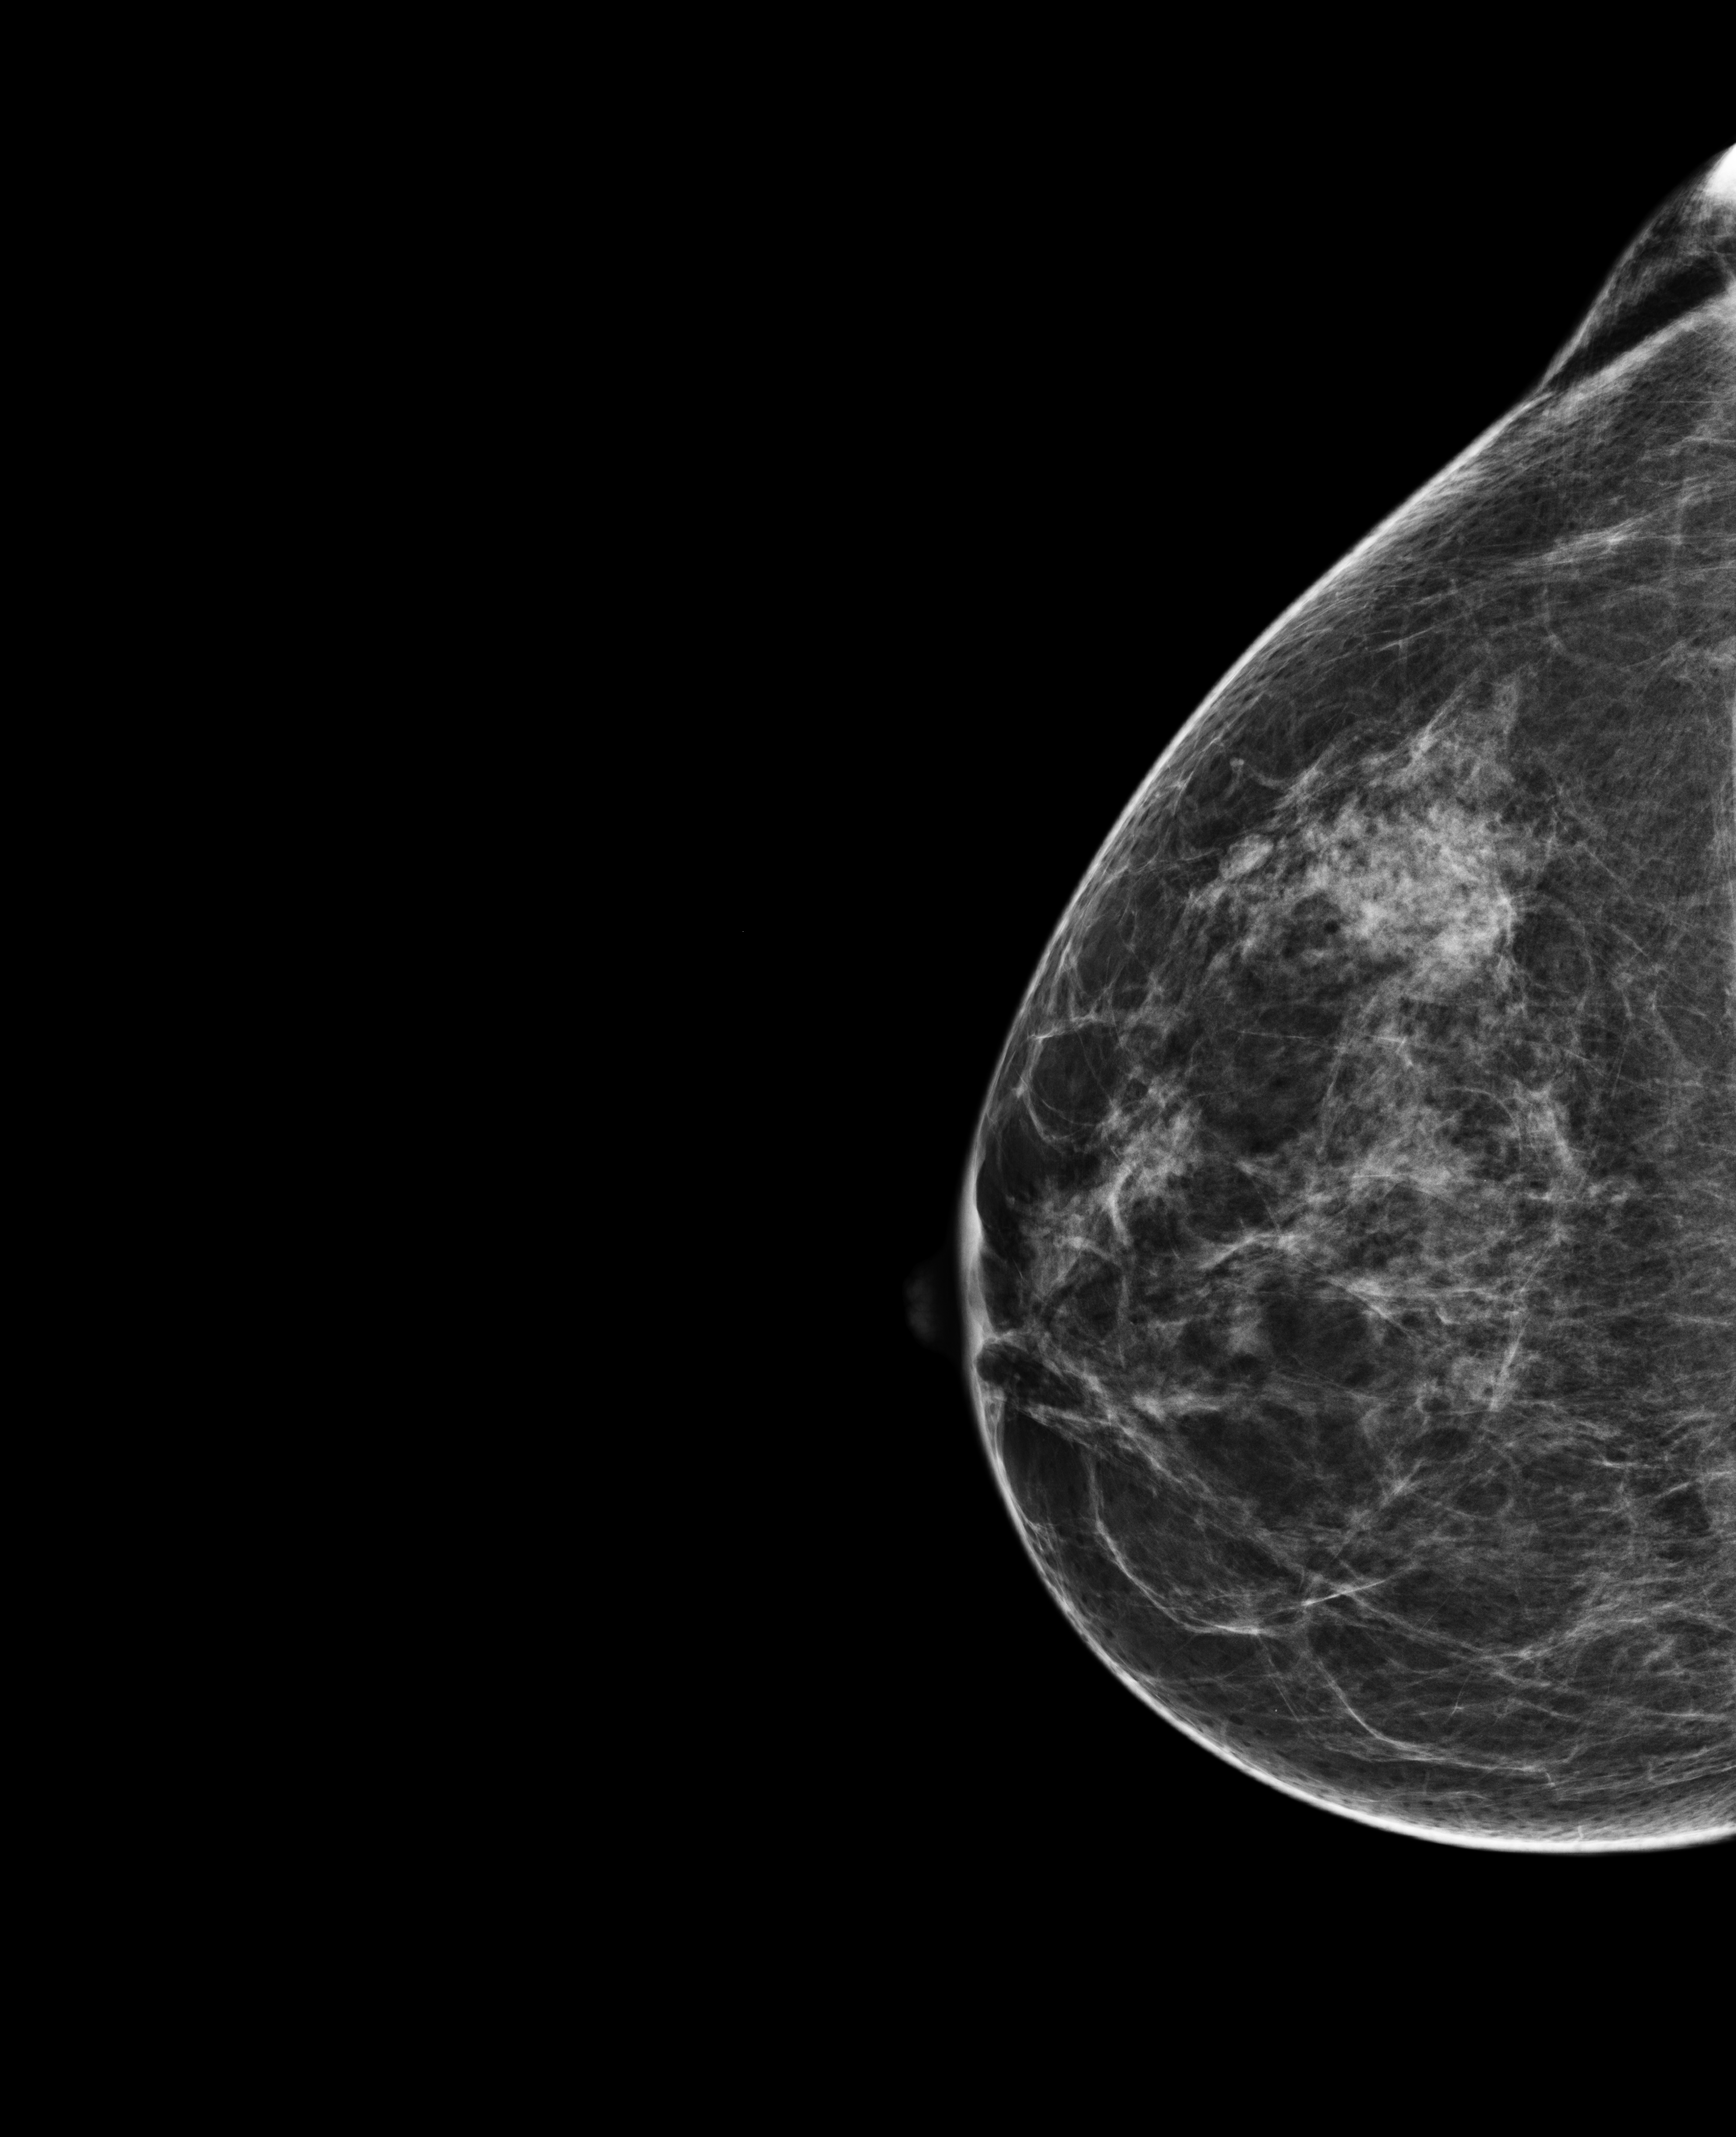
Annual screening mammography examination; system: Selenia Dimensions. Female patient, age 52 years.
Image type: full-field digital mammogram. Breast: right. Projection: exaggerated CC view (lateral).